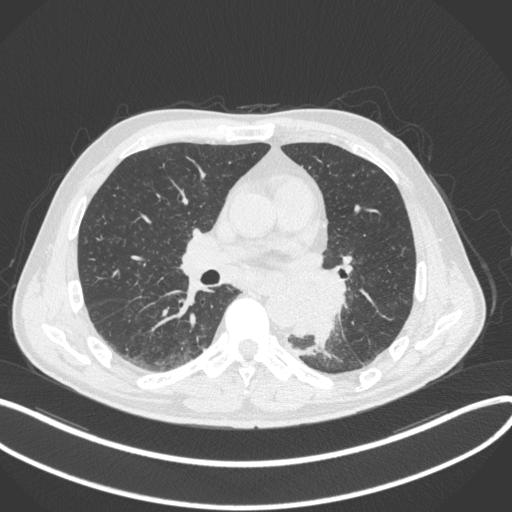
Chest CT, one axial slice. Position 175 of 328 along the scan axis. Reconstruction kernel B31f. 120 kVp. Lung window (W 1500 / L -600 HU). 512 × 512 image matrix. Patient: male, 59 years. Case-level facts recorded for this patient, not image findings: clinical TNM (as recorded): T2a N2 M0.
Structures marked on this image (rectangle marked by the reading radiologist):
- lung tumour (recorded histology: squamous cell carcinoma): bounding box (x1, y1, x2, y2) in pixels: (284, 267, 348, 339)